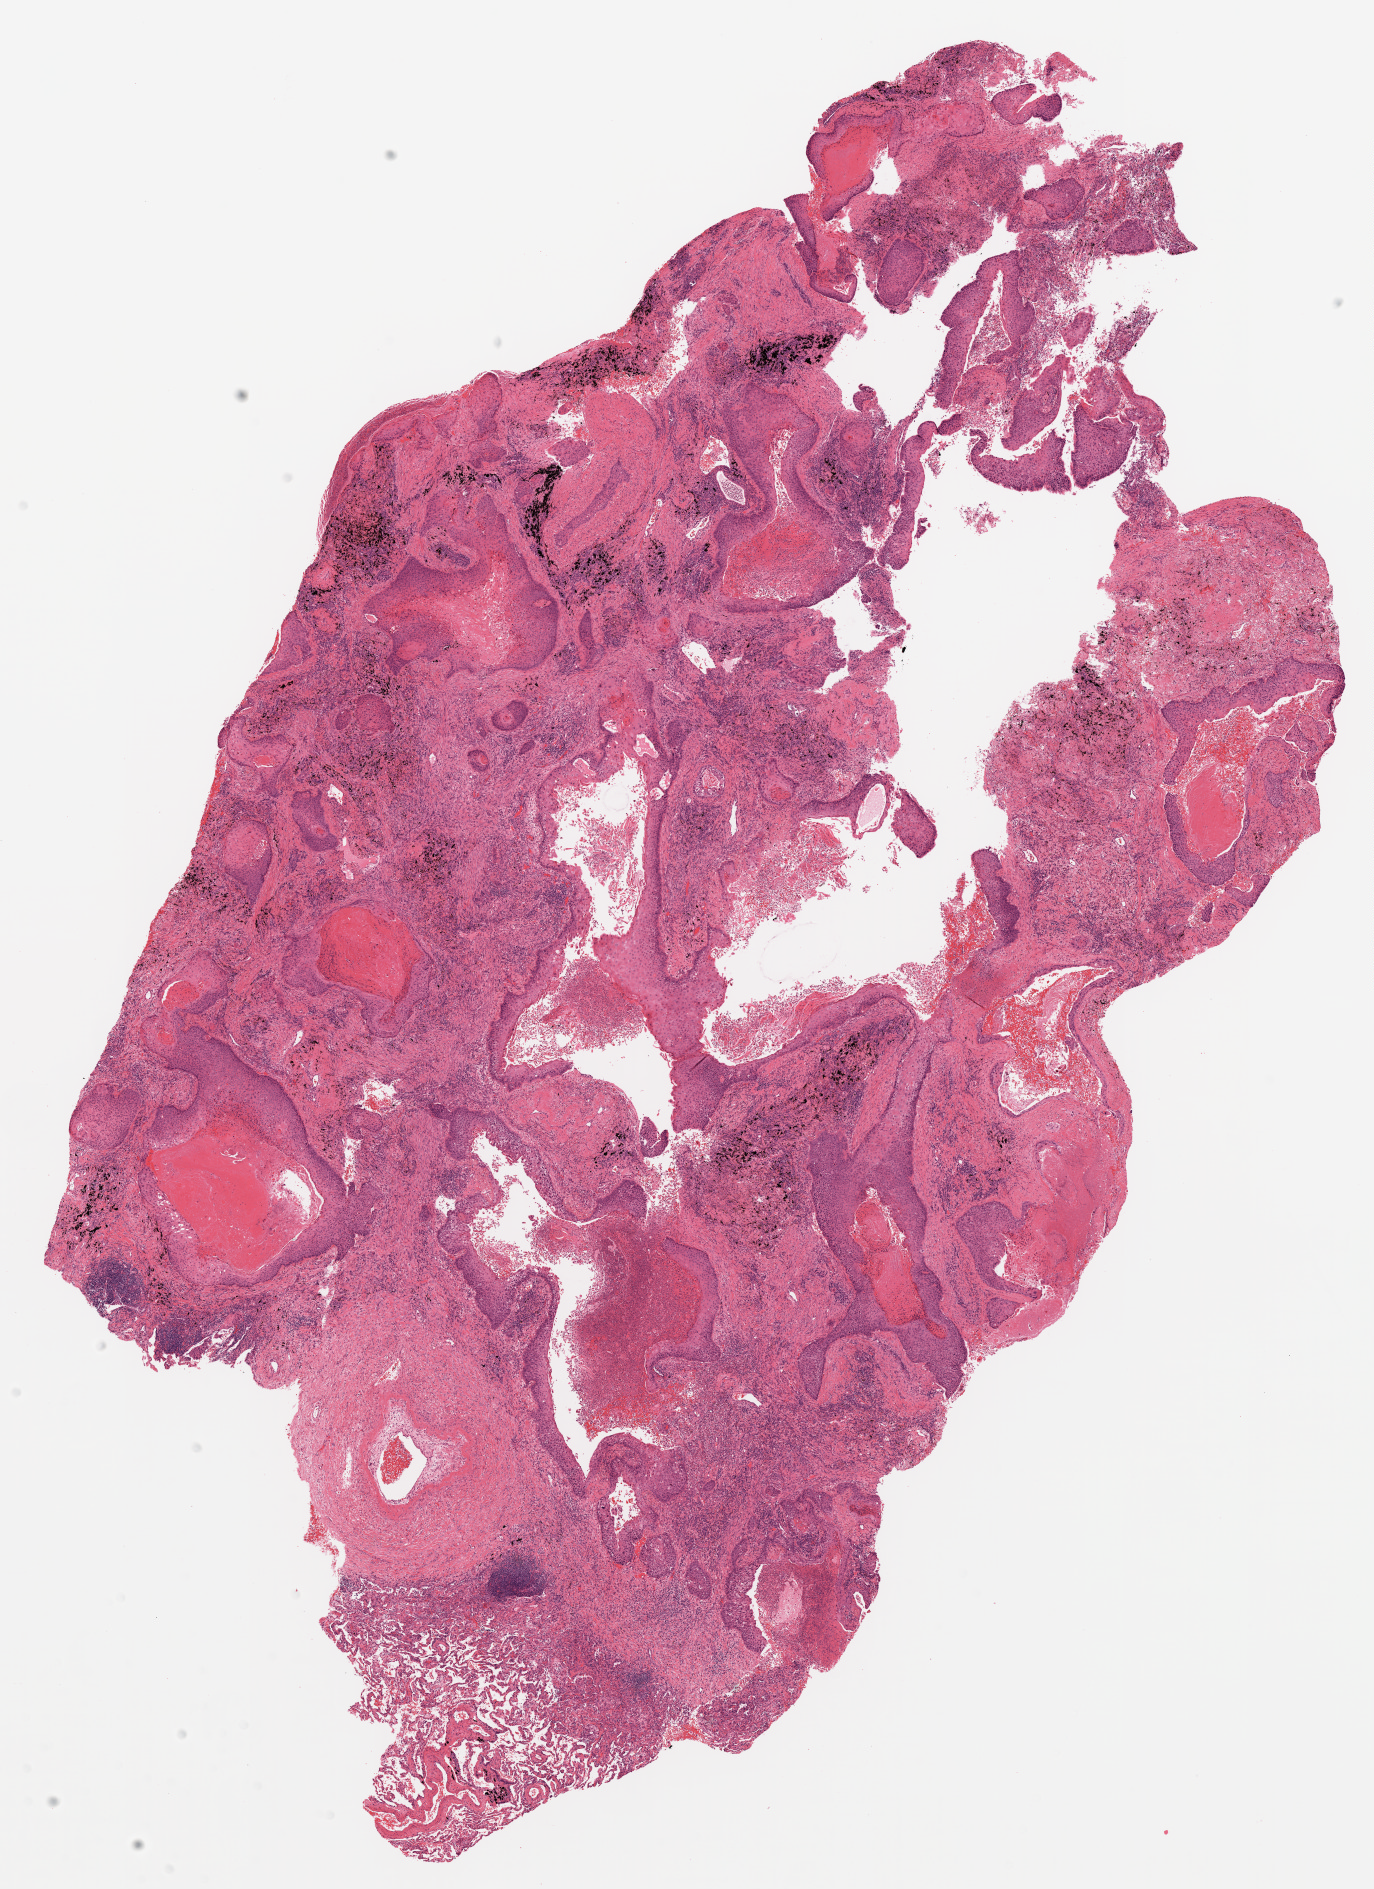
Hematoxylin and eosin (H&E) stained whole-slide image, shown as a low-resolution overview of the whole scanned area (about 11.0 x 15.1 mm); FFPE section; primary tumour sample from the lung. Patient: male, age at initial diagnosis 68 years.
Laterality: left. Diagnosis: Squamous cell carcinoma, NOS (lower lobe, lung). AJCC pathologic stage: IB (6th edition).